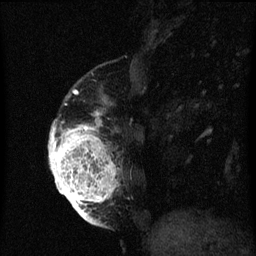
Breast MRI (dynamic contrast-enhanced), one sagittal slice; dynamic contrast-enhanced series, image 2 of 3 at this slice position (ordered by acquisition); 1.5 T; TE 4.2 ms, TR 8 ms; 2 mm slice thickness; 256 × 256 image matrix, field of view 180 × 180 mm. Patient: female, 56 years.
Annotated regions visible in this slice (semi-automatically segmented with operator editing):
- analysis volume of interest (the breast-tissue region the enhancement analysis was run in; not a lesion): bounding box (x1, y1, x2, y2) in pixels: (50, 96, 123, 219)
- tumour enhancement mask (voxels above the 70 % enhancement threshold inside the analysis volume of interest): (50, 112, 117, 219)